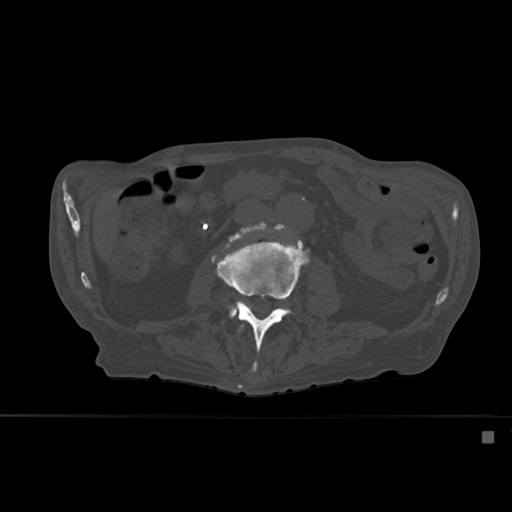
CT including the spine, one axial slice. Position 212 of 527 along the scan axis. Bone window (W 1800 / L 400 HU). 1.5 mm slice thickness. 512 × 512 image matrix, field of view 373 × 373 mm. Patient: male, 78 years. From the clinical record (not read from this slice): primary cancer: prostate.
Structures marked on this image (semi-automatically segmented with operator editing):
- L2 vertebra: bounding box <238,323,244,333> (left, top, right, bottom; pixels)
- L3 vertebra: <211,230,309,372>
- L4 vertebra: <227,227,284,318>